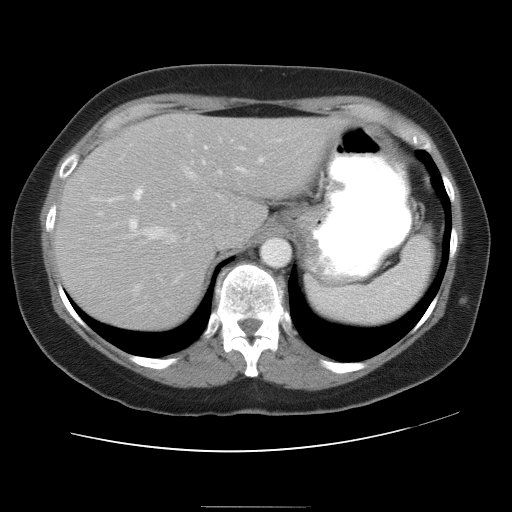
Contrast-enhanced abdominal CT, one axial slice. Position 24 of 30 along the scan axis. Reconstruction kernel STANDARD. Soft-tissue window (W 400 / L 40 HU). 512 × 512 image matrix. Female patient, age 52 years. Case-level facts recorded for this patient, not image findings: diagnosis: colorectal cancer liver metastases, imaged before liver resection; multiple liver metastases: no; largest metastasis: 3 cm.
Annotated regions visible in this slice (expert manual segmentation):
- hepatic veins: bounding box <80,158,264,242> (left, top, right, bottom; pixels)
- liver: <55,115,331,332>
- planned liver remnant (the part of the liver to remain after resection): <152,114,331,226>
- portal vein (with intrahepatic branches): <129,140,243,234>